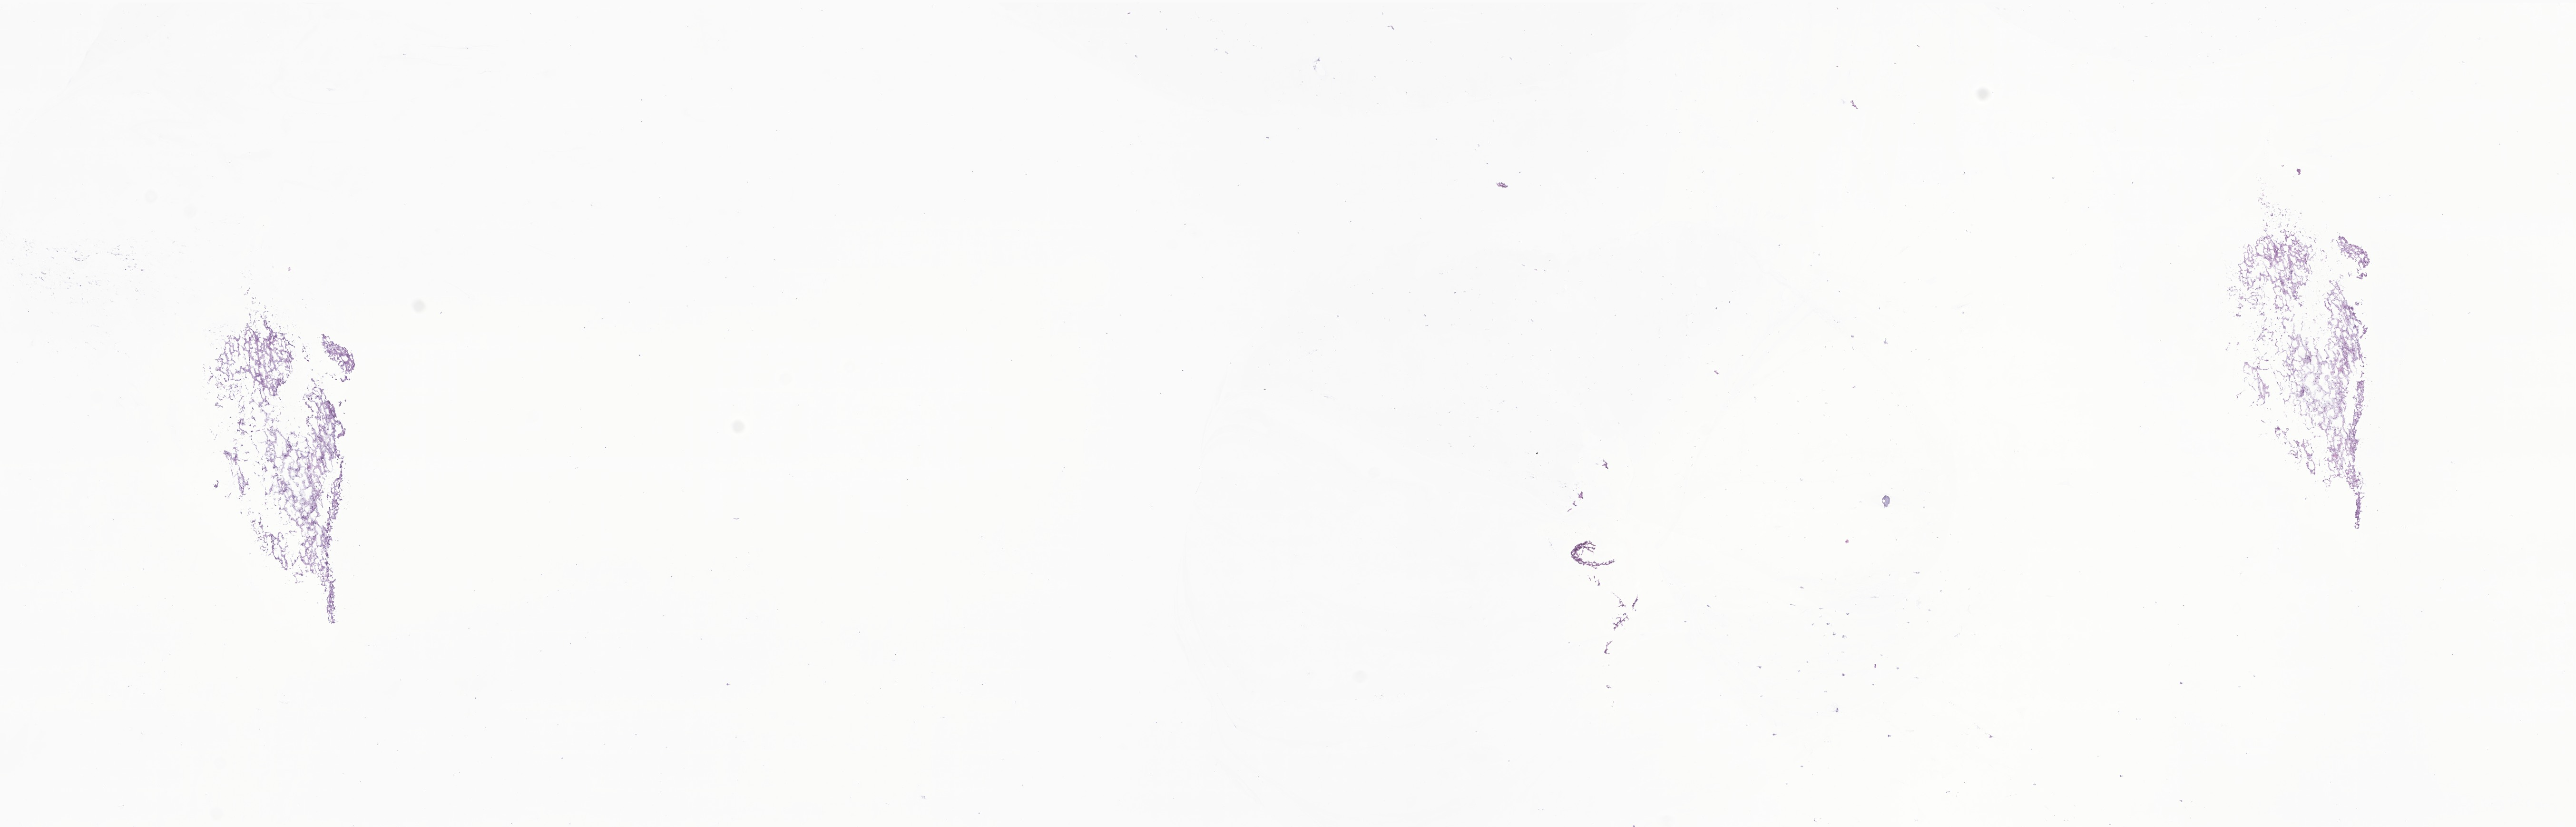
Whole-slide image, hematoxylin and eosin (H&E) stain of tumor tissue from the brain stem, a low-resolution overview of the entire scanned area, about 22.8 x 7.3 mm. Frozen section (OCT-embedded). Patient: male, age 46 months (3 years 10 months).
• diagnosis (ICD-O-3 morphology term): Glioma, malignant